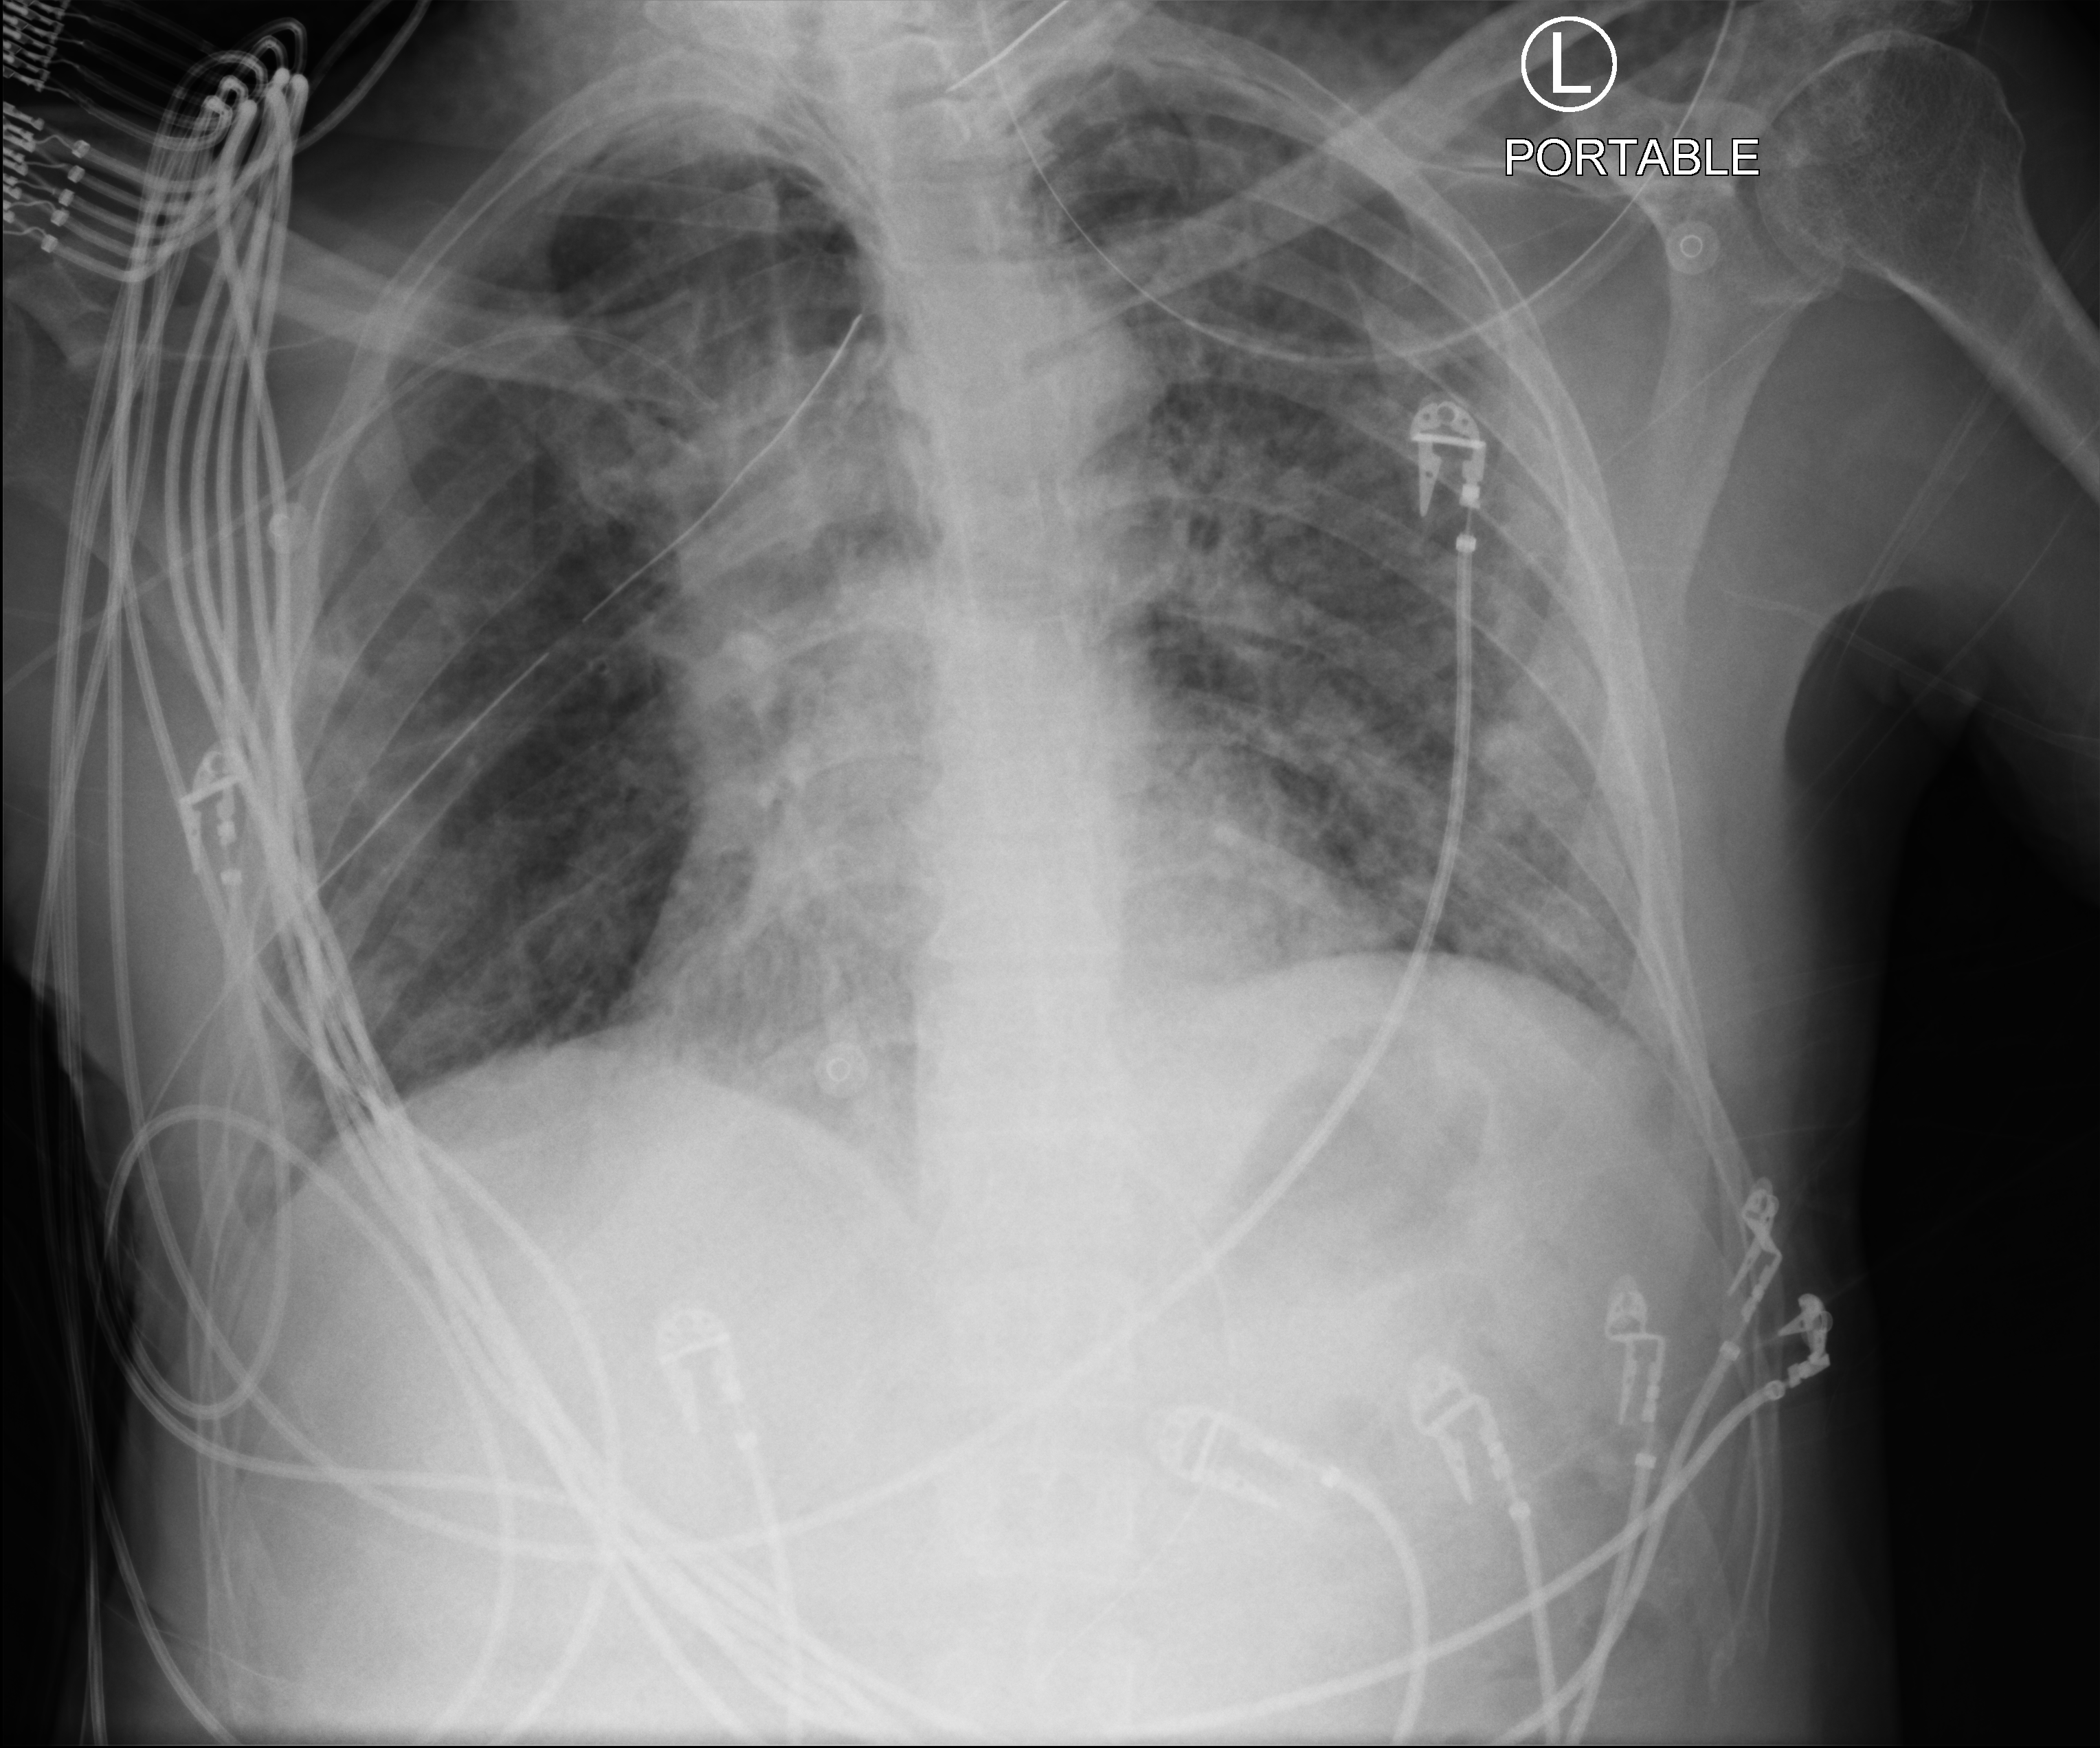
Portable chest radiograph, anteroposterior (AP) projection. Male patient hospitalised with COVID-19, age 18–59 years.
Hospital-stay facts (about this admission, not read from this image; timing relative to this image not recorded): chronic kidney disease (admission record): no.